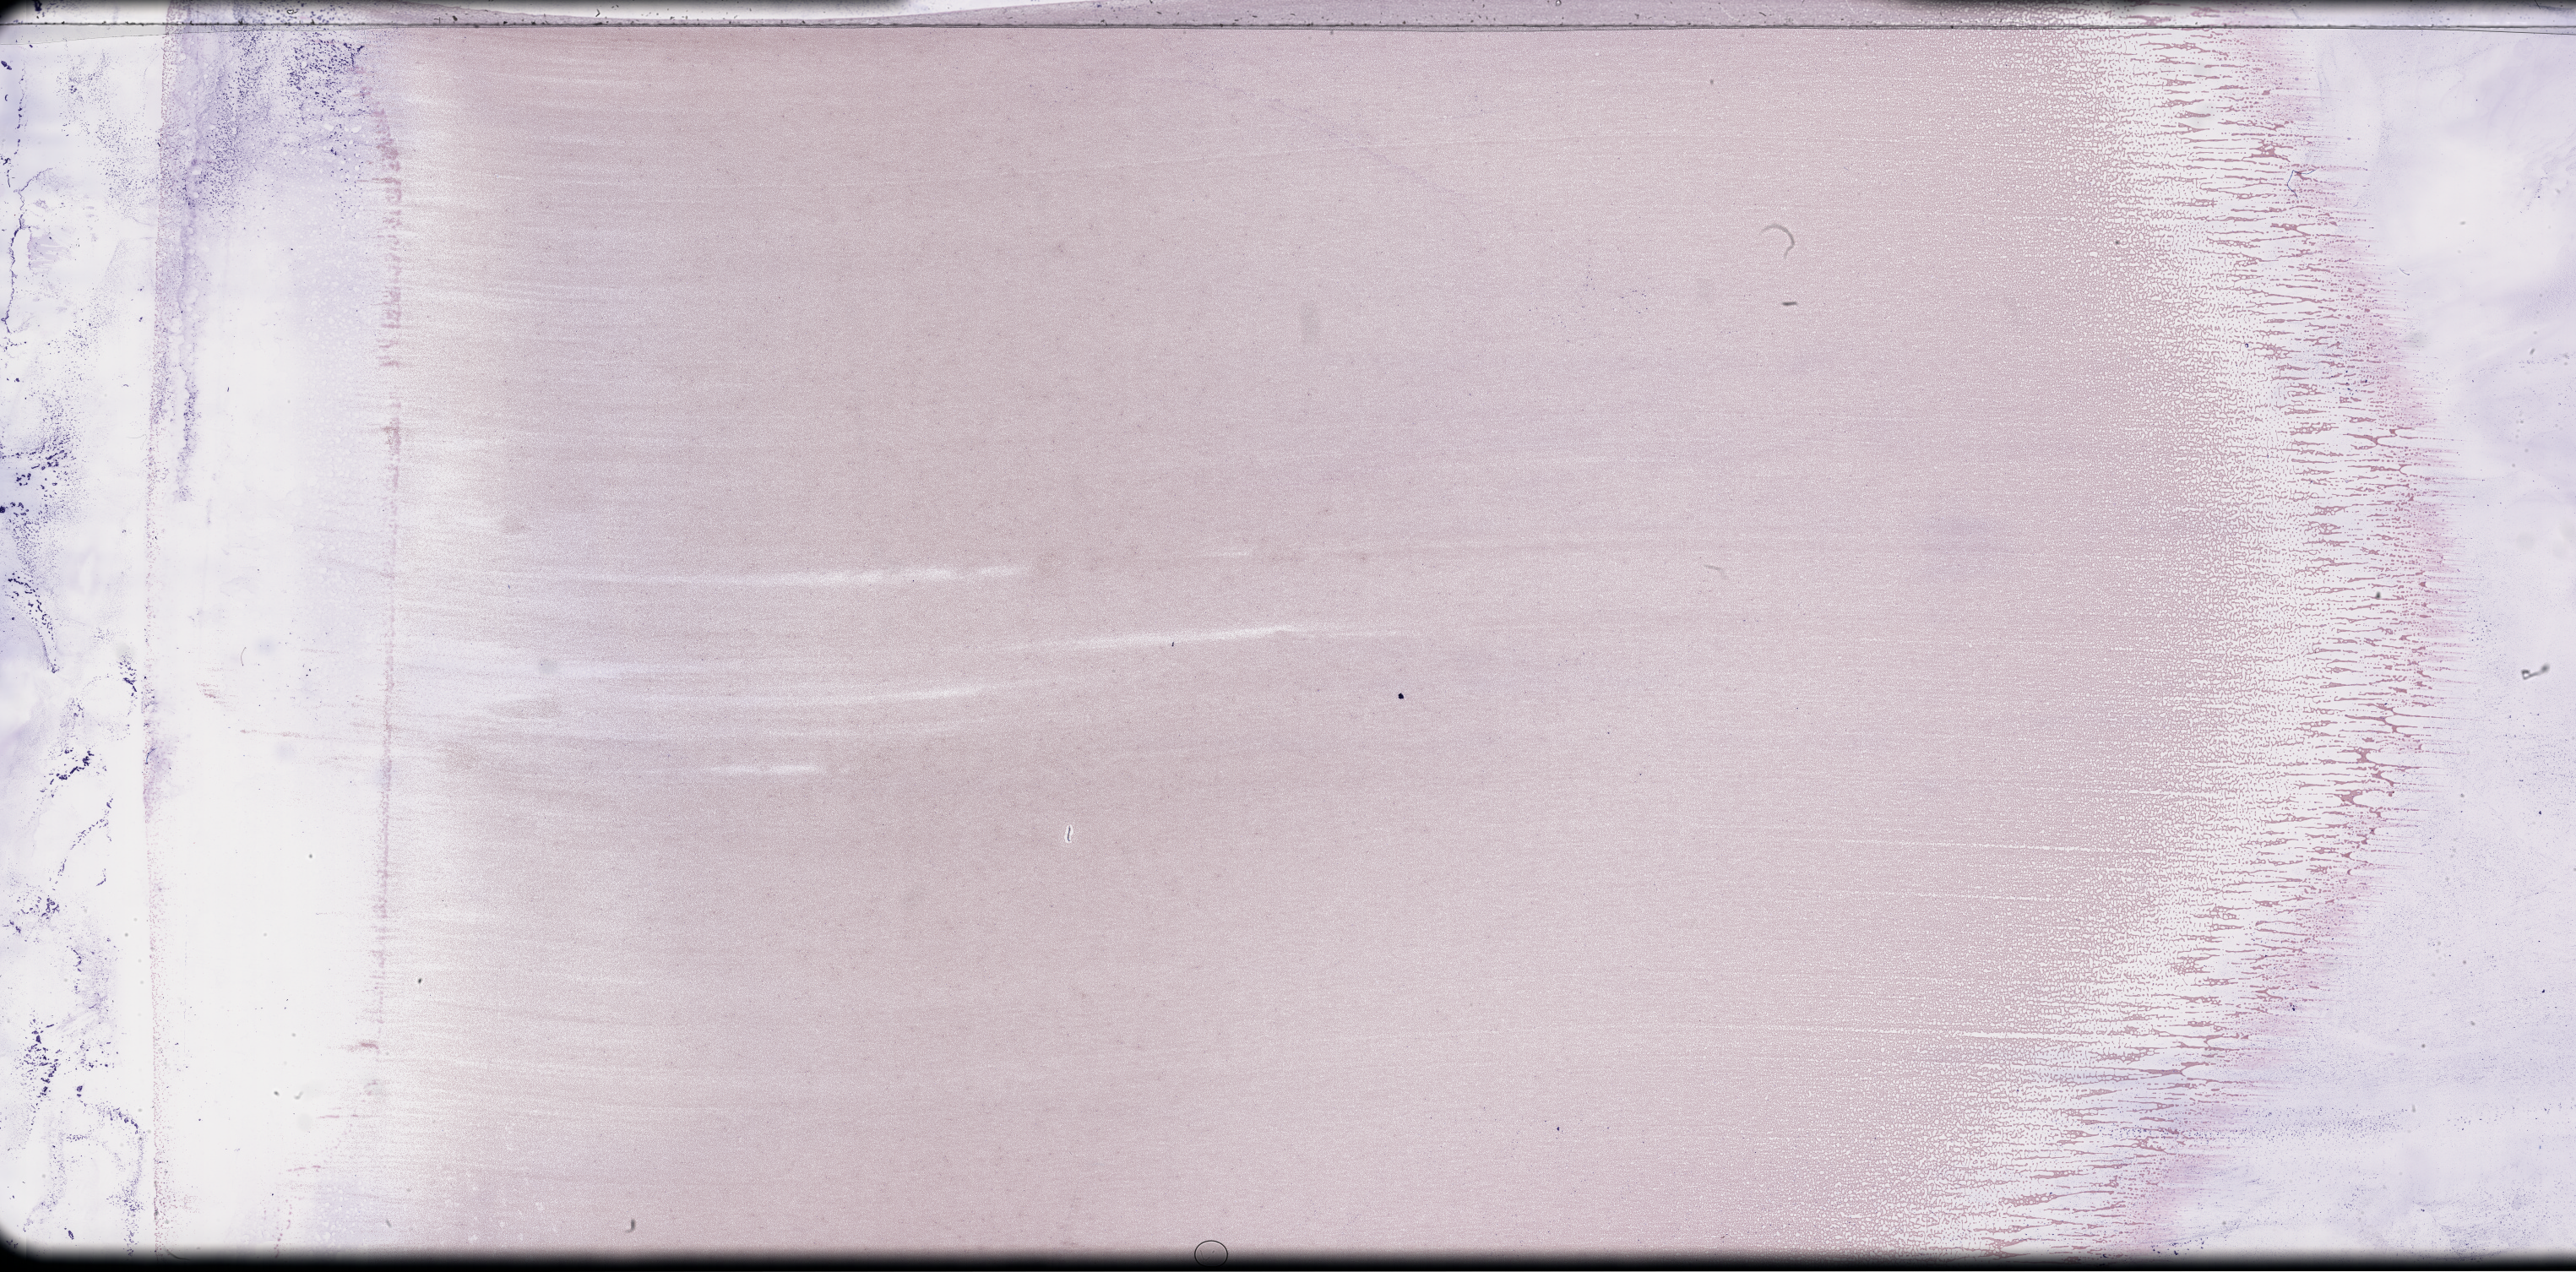
Wright-Giemsa-stained whole blood smear, whole-slide image — low-resolution overview of the scanned area, about 49.3 x 24.3 mm. Smear from an EDTA sample. Specimen time point: collected on treatment. Patient: female.
Patient diagnosis: Plasma Cell Myeloma.